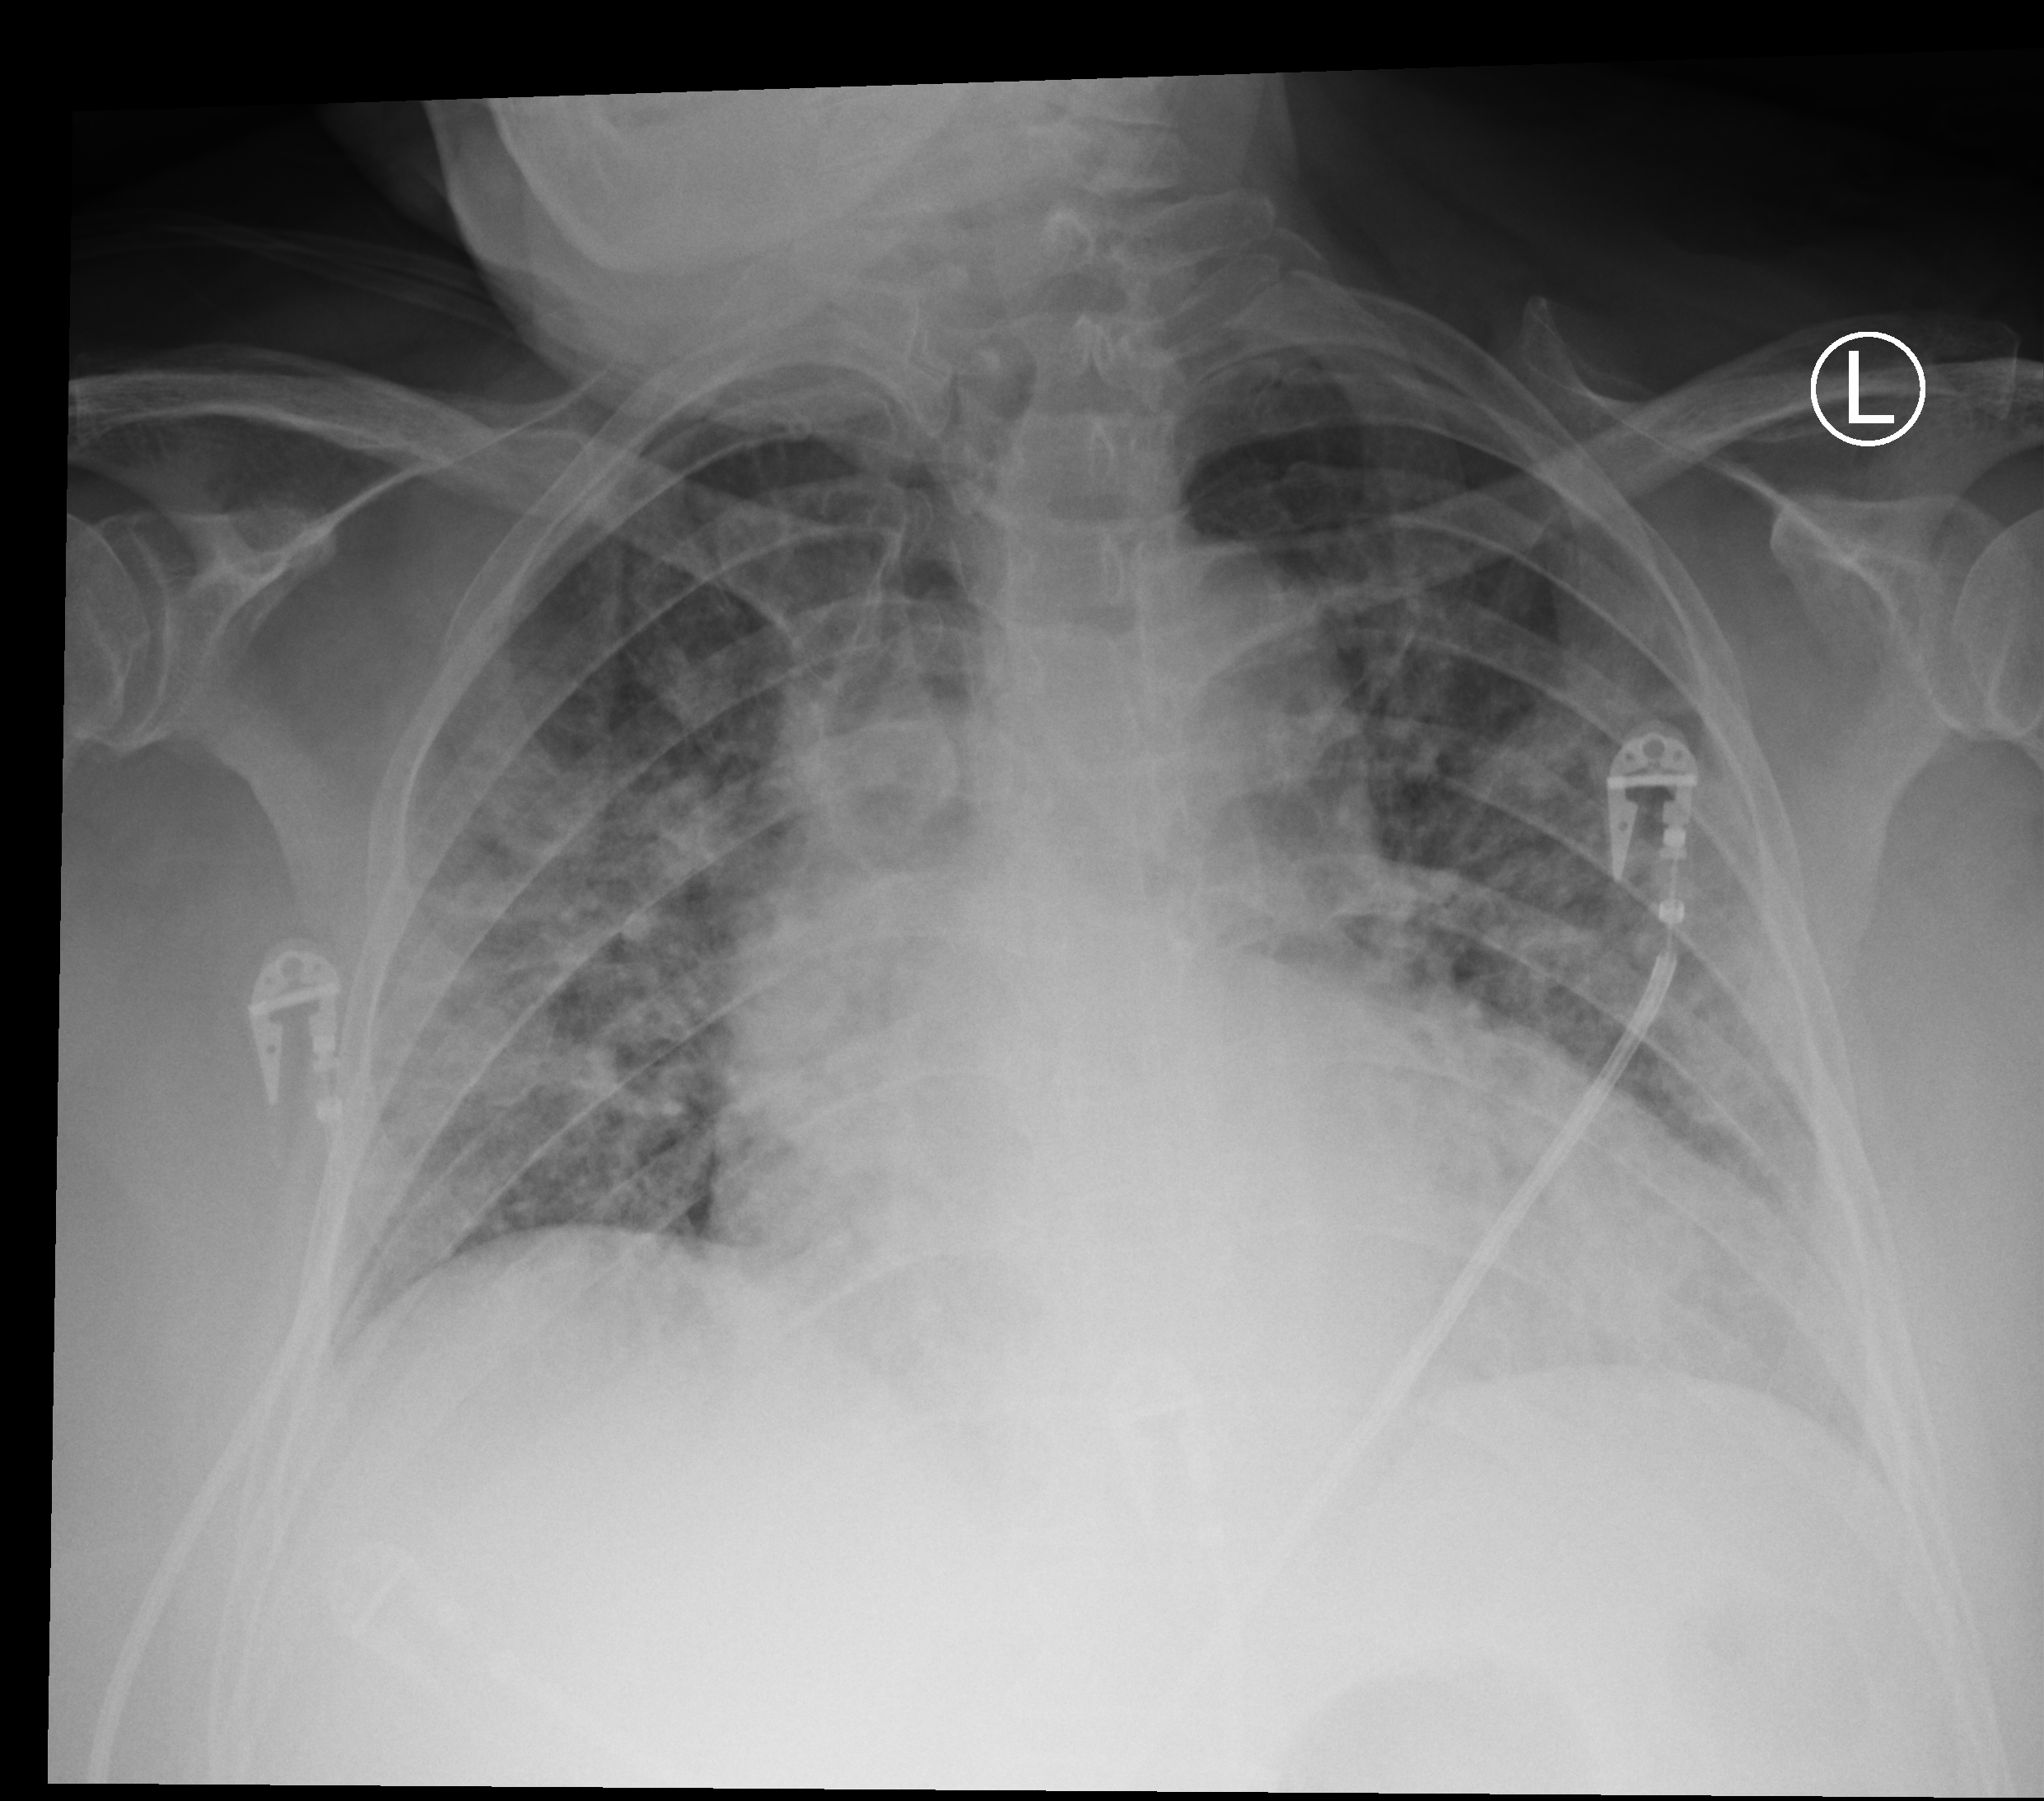
Portable chest radiograph; anteroposterior (AP) projection. Patient hospitalised with COVID-19; female, aged 60–74 years.
From the hospital-stay record, not from the radiograph (when in the stay this image was taken is not recorded):
- admitted to intensive care during this hospital stay: no
- mechanically ventilated during this hospital stay: no
- diabetes (admission record): yes